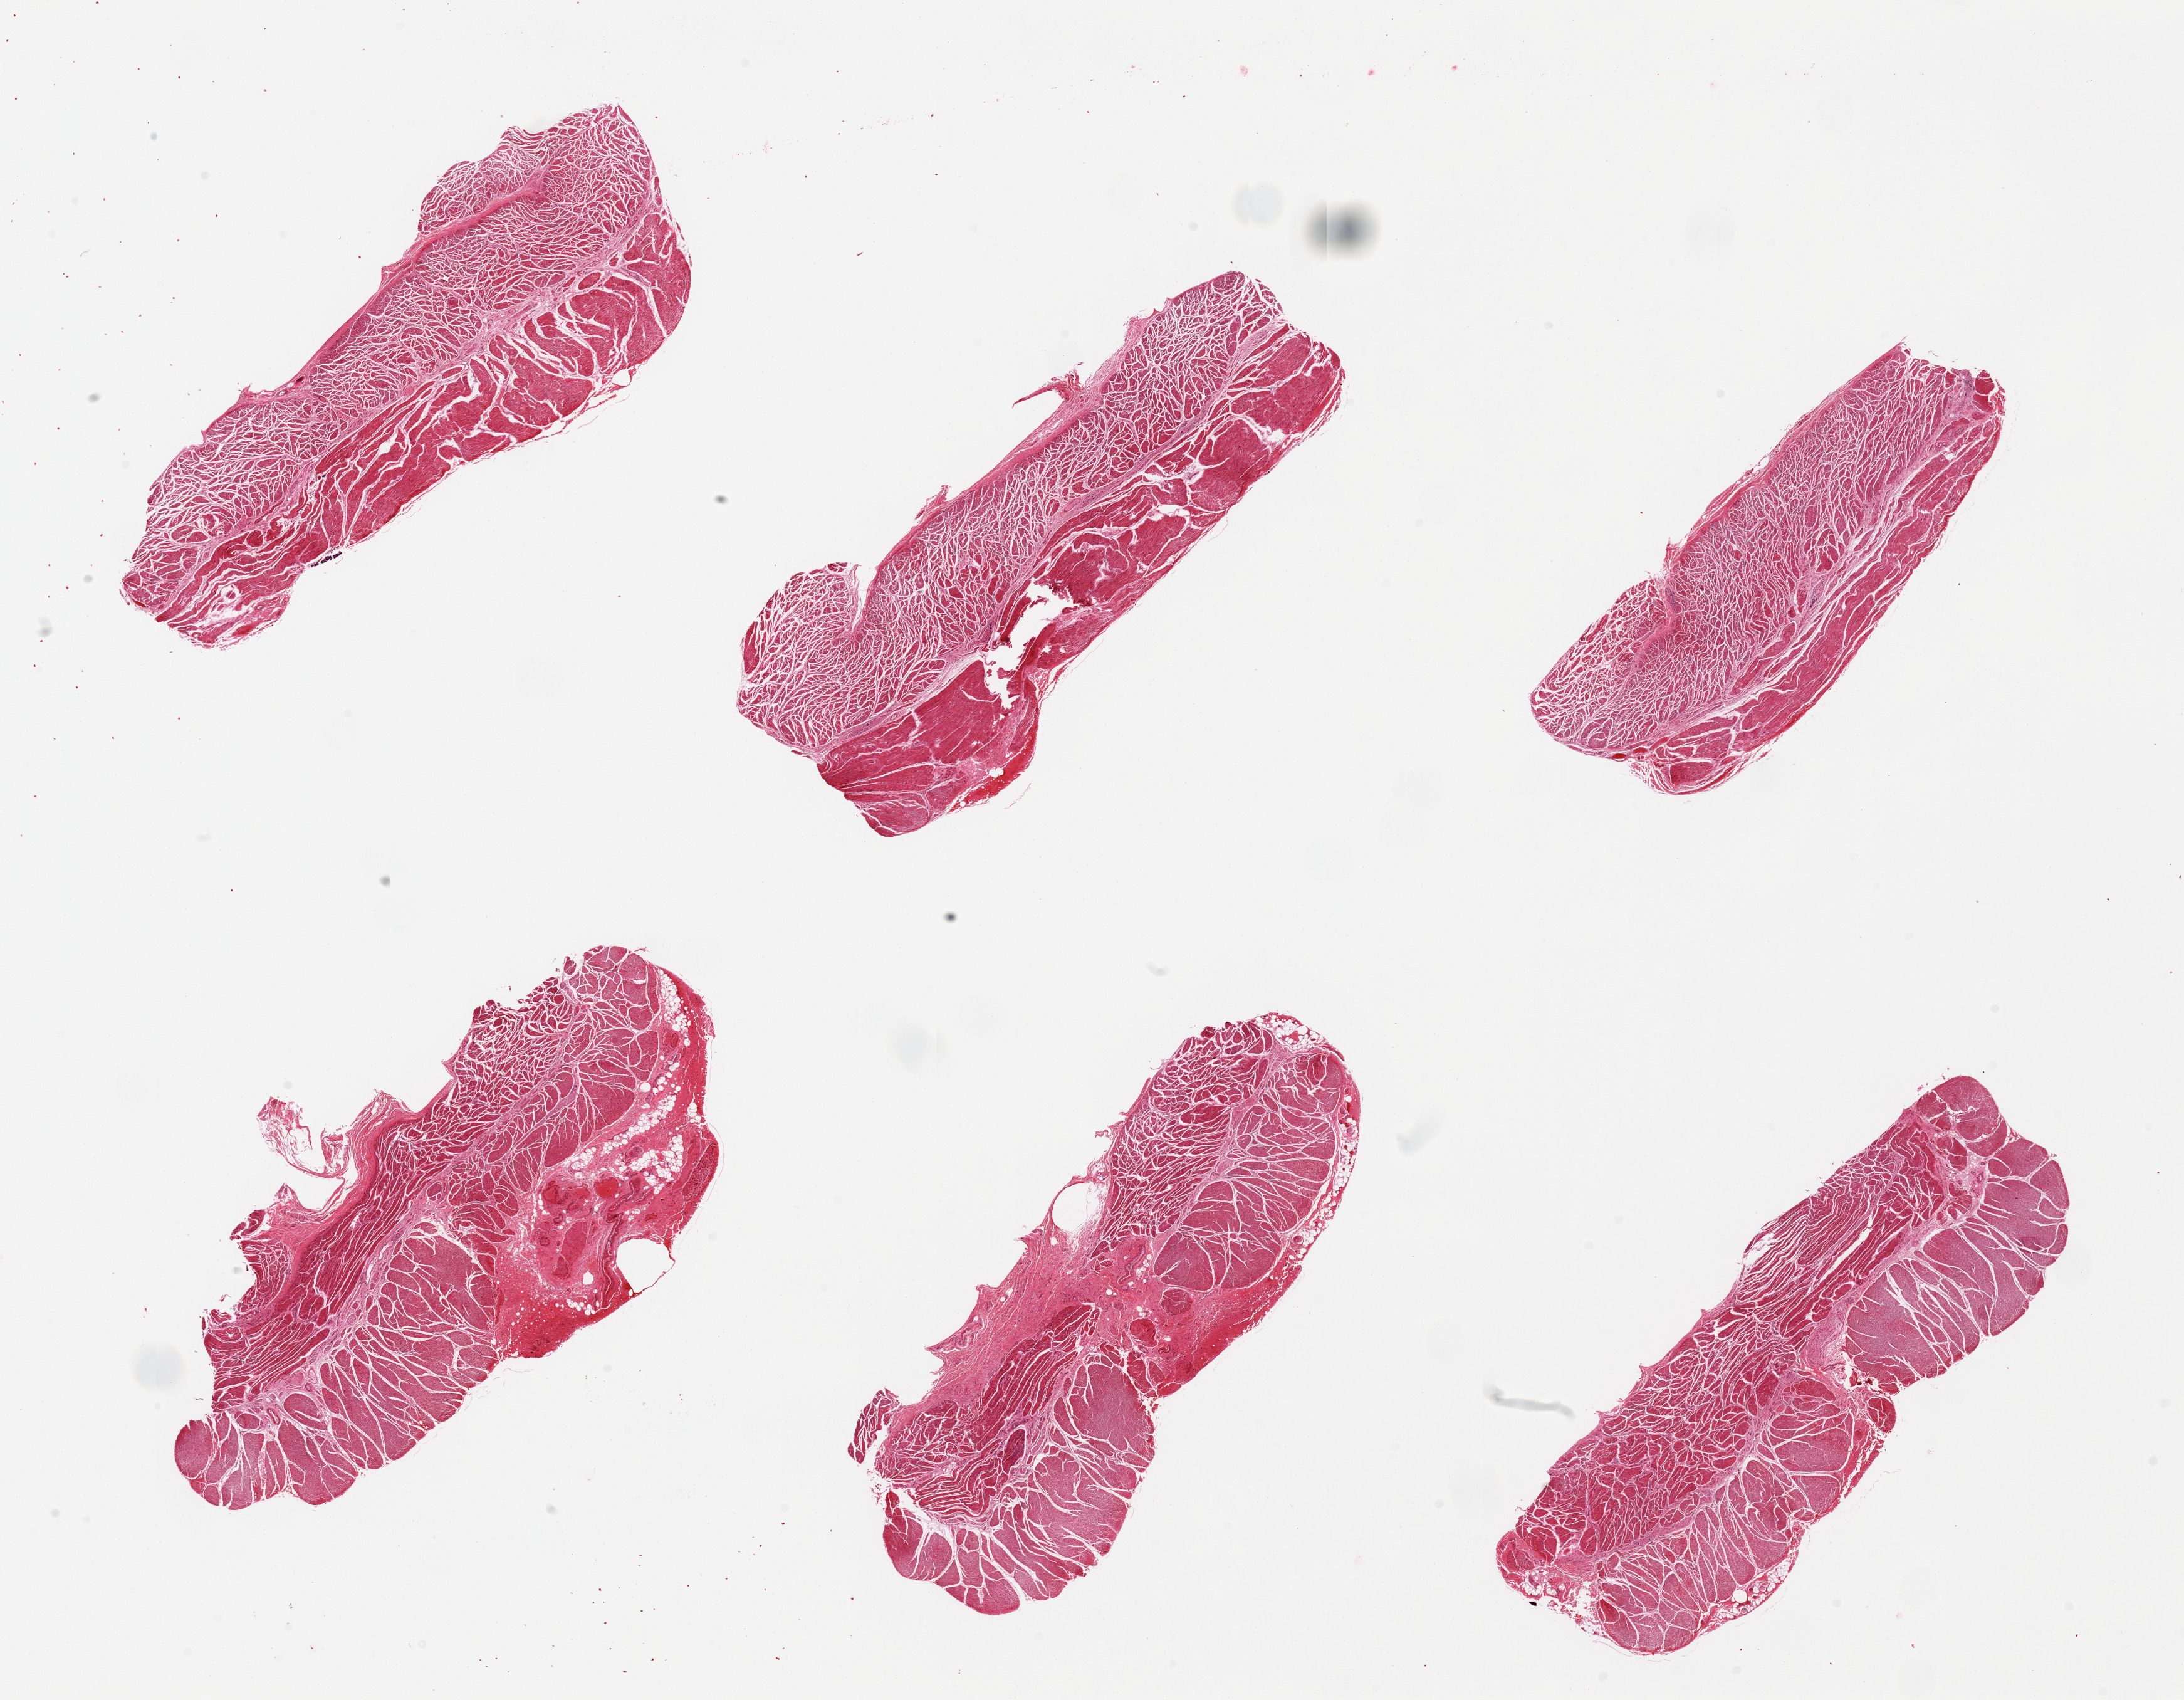
Digitized haematoxylin and eosin-stained section, a low-resolution overview of the entire scanned area, about 27.6 x 21.5 mm, PAXgene-fixed, paraffin-embedded tissue, sampled site (target tissue): esophageal muscle, donor tissue sample.
- review note (as recorded): 6 pieces, all muscularis